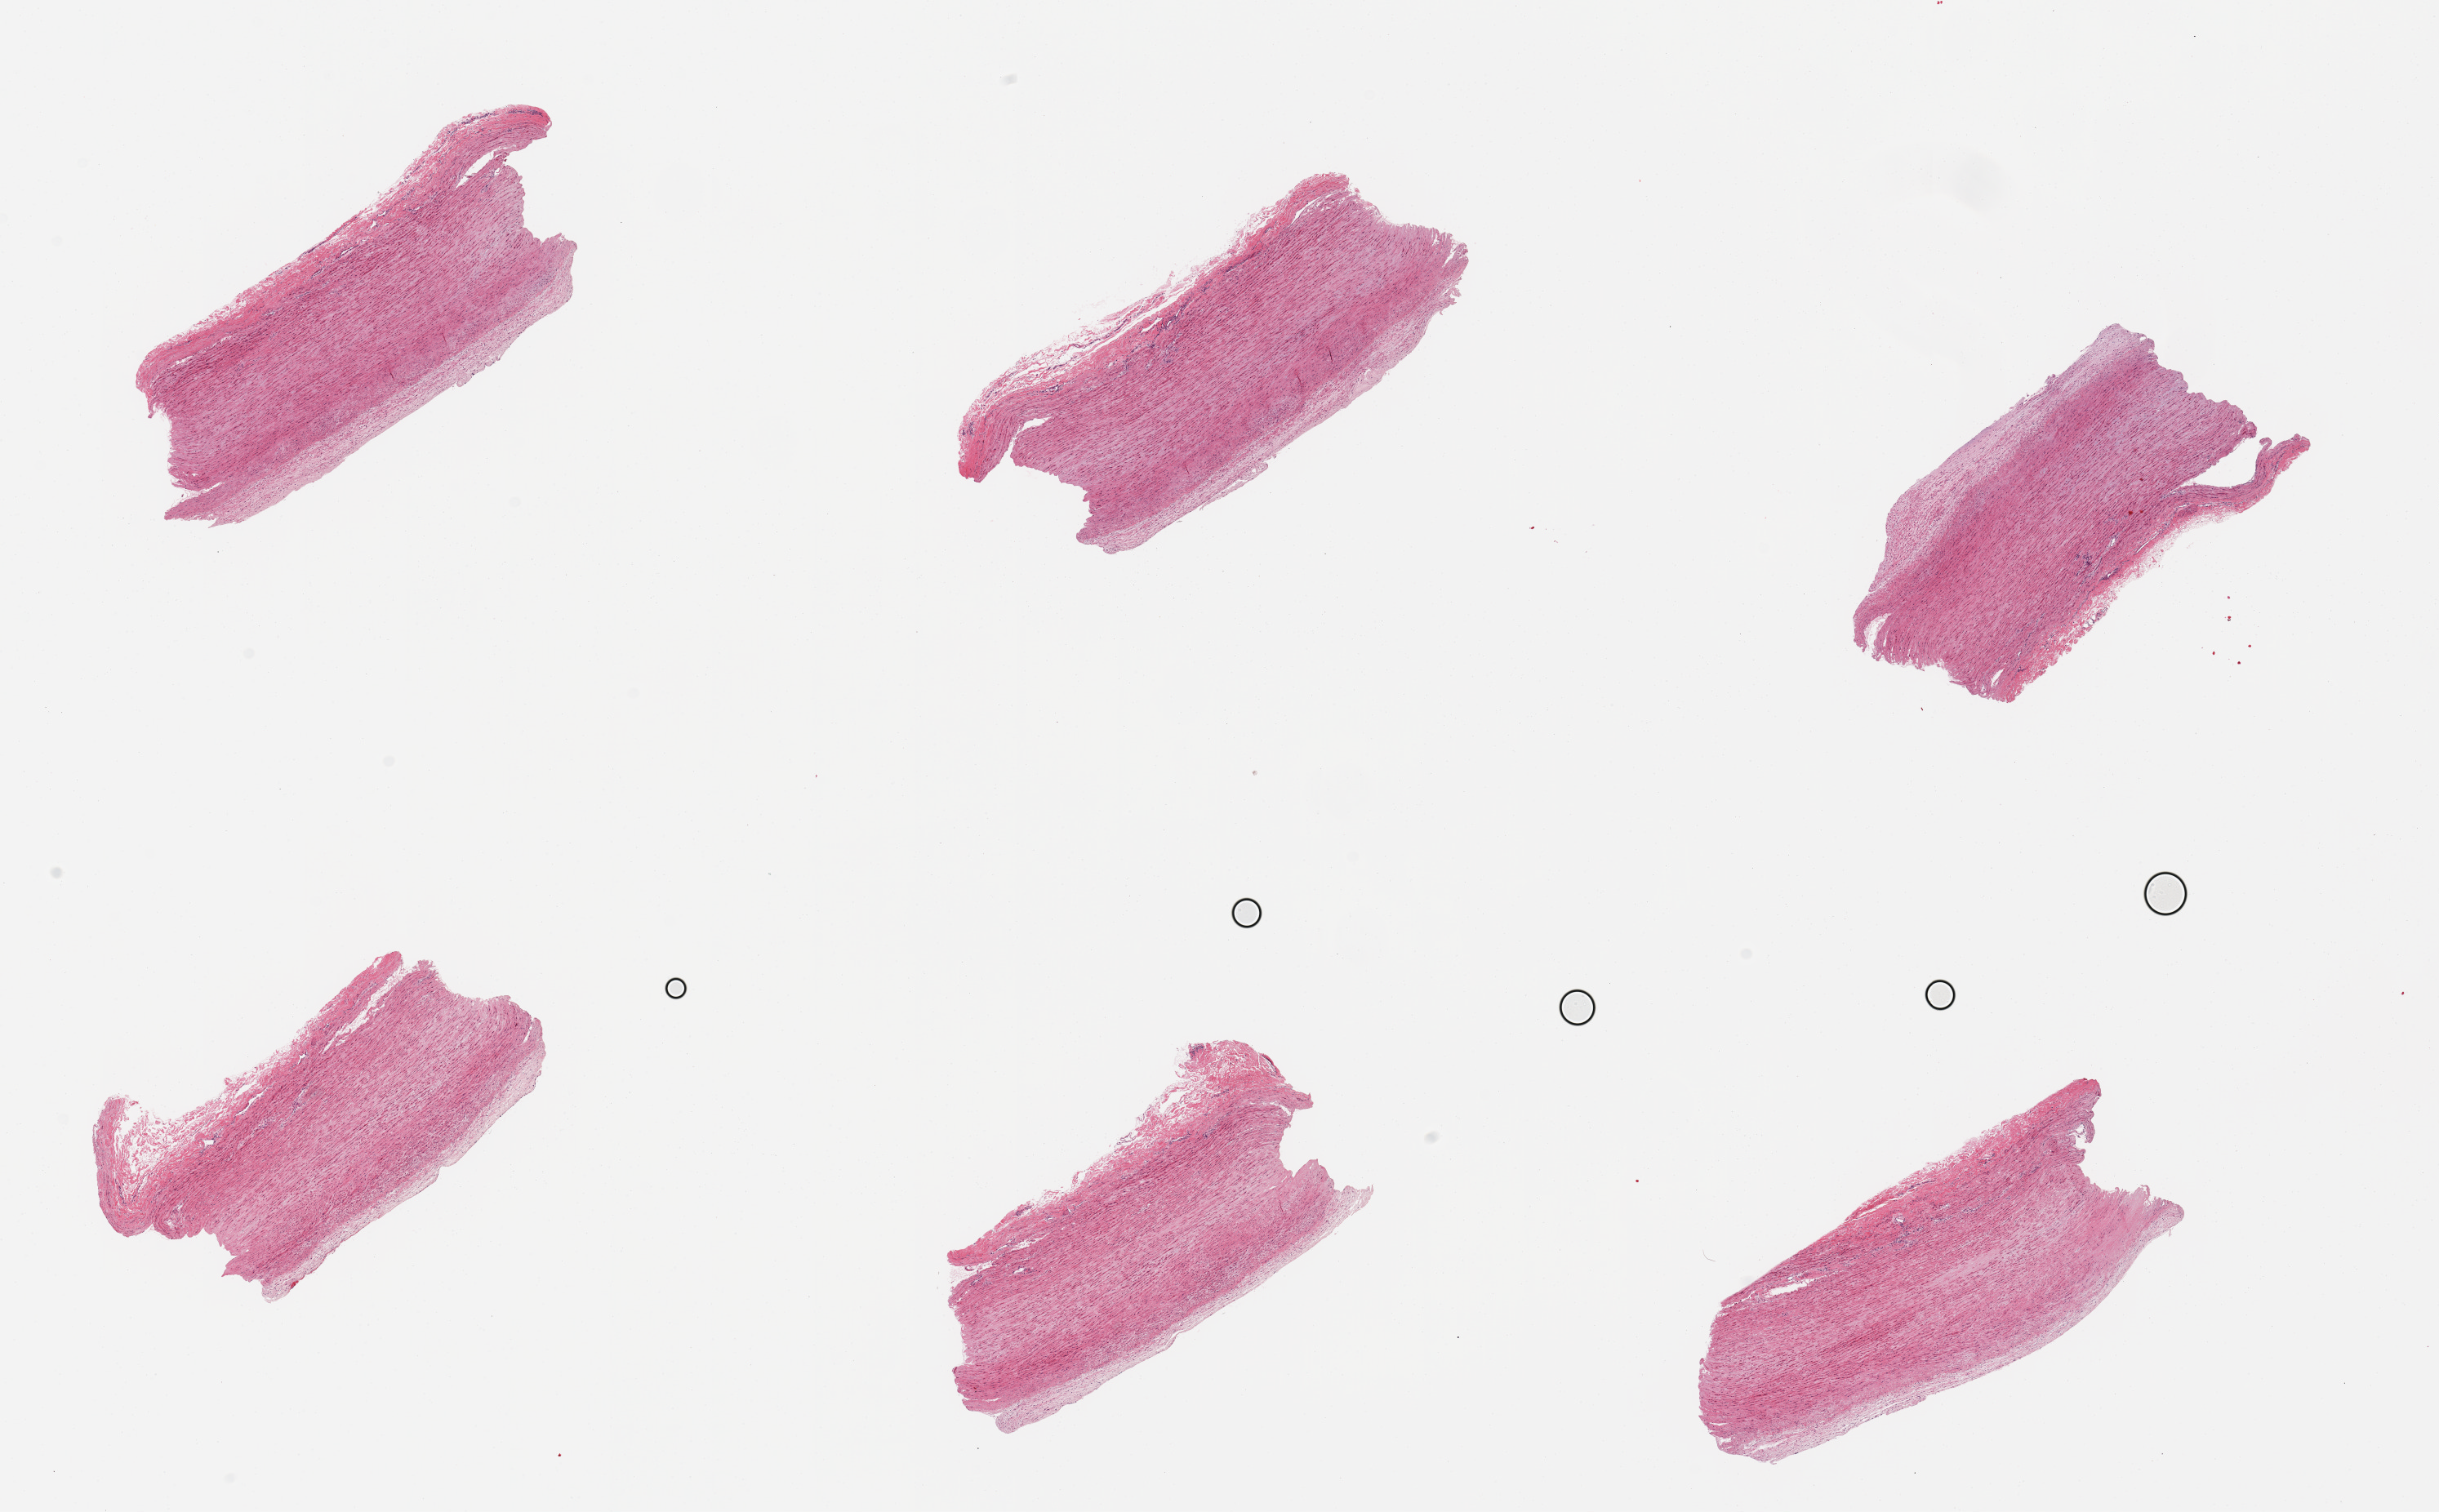
H&E whole-slide image, brightfield, low-resolution overview of the scanned area, about 23.6 x 14.6 mm (slide scanned at 20x); PAXgene-fixed, paraffin-embedded tissue; sampled site (target tissue): aorta; donor tissue sample. Donor sex: male.
Review note (as recorded): 6 pieces; flat sclerotic plaques.